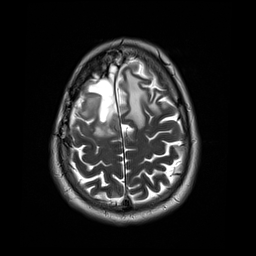
Brain MRI from a brain-tumour surgery series, one axial slice. Position 10 of 44 along the scan axis. 4 mm slice thickness. 256 × 256 image matrix. Case-level facts recorded for this patient, not image findings: histopathology: Astrocytoma; WHO grade: 4; IDH mutation: yes; tumour location: Right Frontal.
Outlined on this slice (outlined manually by an expert reader):
- tumour: bounding box [x1, y1, x2, y2] px = [81, 94, 116, 138]